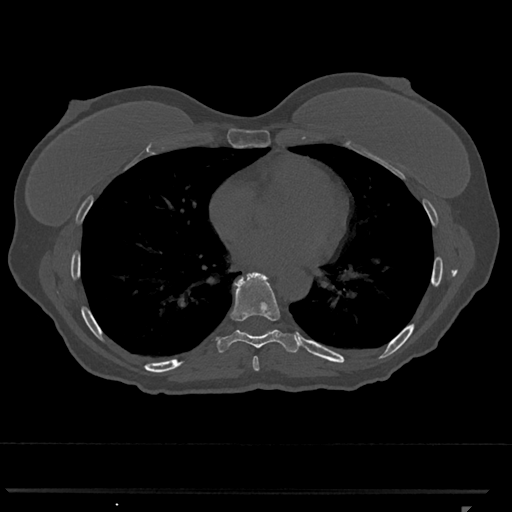
CT including the spine, one axial slice. Position 664 of 793 along the scan axis. Reconstruction kernel Br40s/3. Bone window (W 1800 / L 400 HU). 0.5 mm slice thickness. 512 × 512 image matrix. Female patient, age 62 years. Case-level facts recorded for this patient, not image findings: primary cancer: renal.
Structures marked on this image (semi-automatic segmentation, software-assisted and operator-edited):
- T7 vertebra: bounding box [x1, y1, x2, y2] px = [252, 356, 260, 371]
- T8 vertebra: [217, 272, 302, 353]